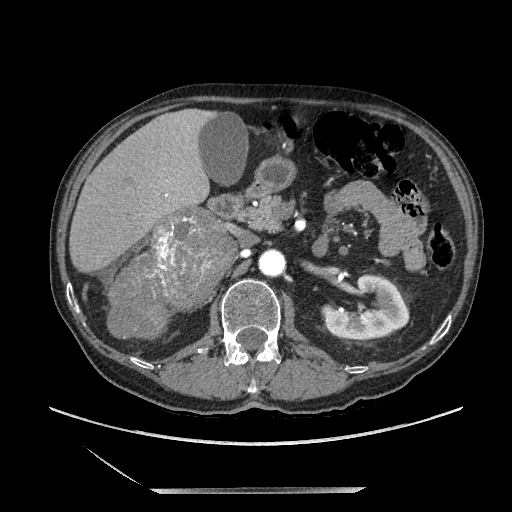
Contrast-enhanced abdominal CT, one axial slice; position 105 of 243 along the scan axis; soft-tissue window (W 400 / L 40 HU); 1.25 mm slice thickness; 512 × 512 image matrix. Male patient. Case-level facts recorded for this patient, not image findings: diagnosis: adrenocortical carcinoma; tumour side: right adrenal; tumour size at pathology: 16 cm; Ki-67 index: 17 %; stage (as recorded): 3.
Annotated regions visible in this slice (semi-automatically segmented with operator editing):
- mass: bounding box <114,209,232,337> (left, top, right, bottom; pixels)